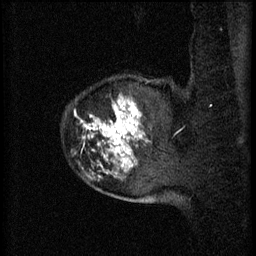
Breast MRI (dynamic contrast-enhanced), one sagittal slice. 3 images stored at this slice position (order not interpretable as contrast timing). 1.5 T. TE 4.2 ms, TR 11 ms. 2 mm slice thickness. 256 × 256 image matrix, field of view 180 × 180 mm. Female patient, age 52 years.
Annotated regions visible in this slice (semi-automatically segmented with operator editing):
- analysis volume of interest (the breast-tissue region the enhancement analysis was run in; not a lesion): bounding box [x1, y1, x2, y2] px = [84, 94, 168, 157]
- tumour enhancement mask (voxels above the 70 % enhancement threshold inside the analysis volume of interest): [86, 100, 141, 153]